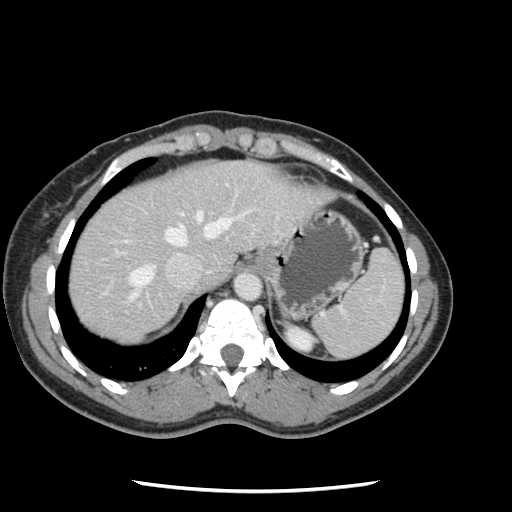
Contrast-enhanced abdominal CT, one axial slice. 120 kVp. Intravenous contrast given. Soft-tissue window (W 400 / L 40 HU). 2.5 mm slice thickness. 512 × 512 image matrix. Female patient, age 43 years. From the clinical record (not read from this slice): diagnosis: colorectal cancer liver metastases, imaged before liver resection; multiple liver metastases: yes; largest metastasis: 3.4 cm; disease in both lobes: yes.
Structures marked on this image (expert manual segmentation):
- hepatic veins: bounding box [x1, y1, x2, y2] px = [129, 210, 245, 300]
- liver: [69, 161, 326, 343]
- planned liver remnant (the part of the liver to remain after resection): [68, 173, 197, 306]
- portal vein (with intrahepatic branches): [114, 233, 253, 307]